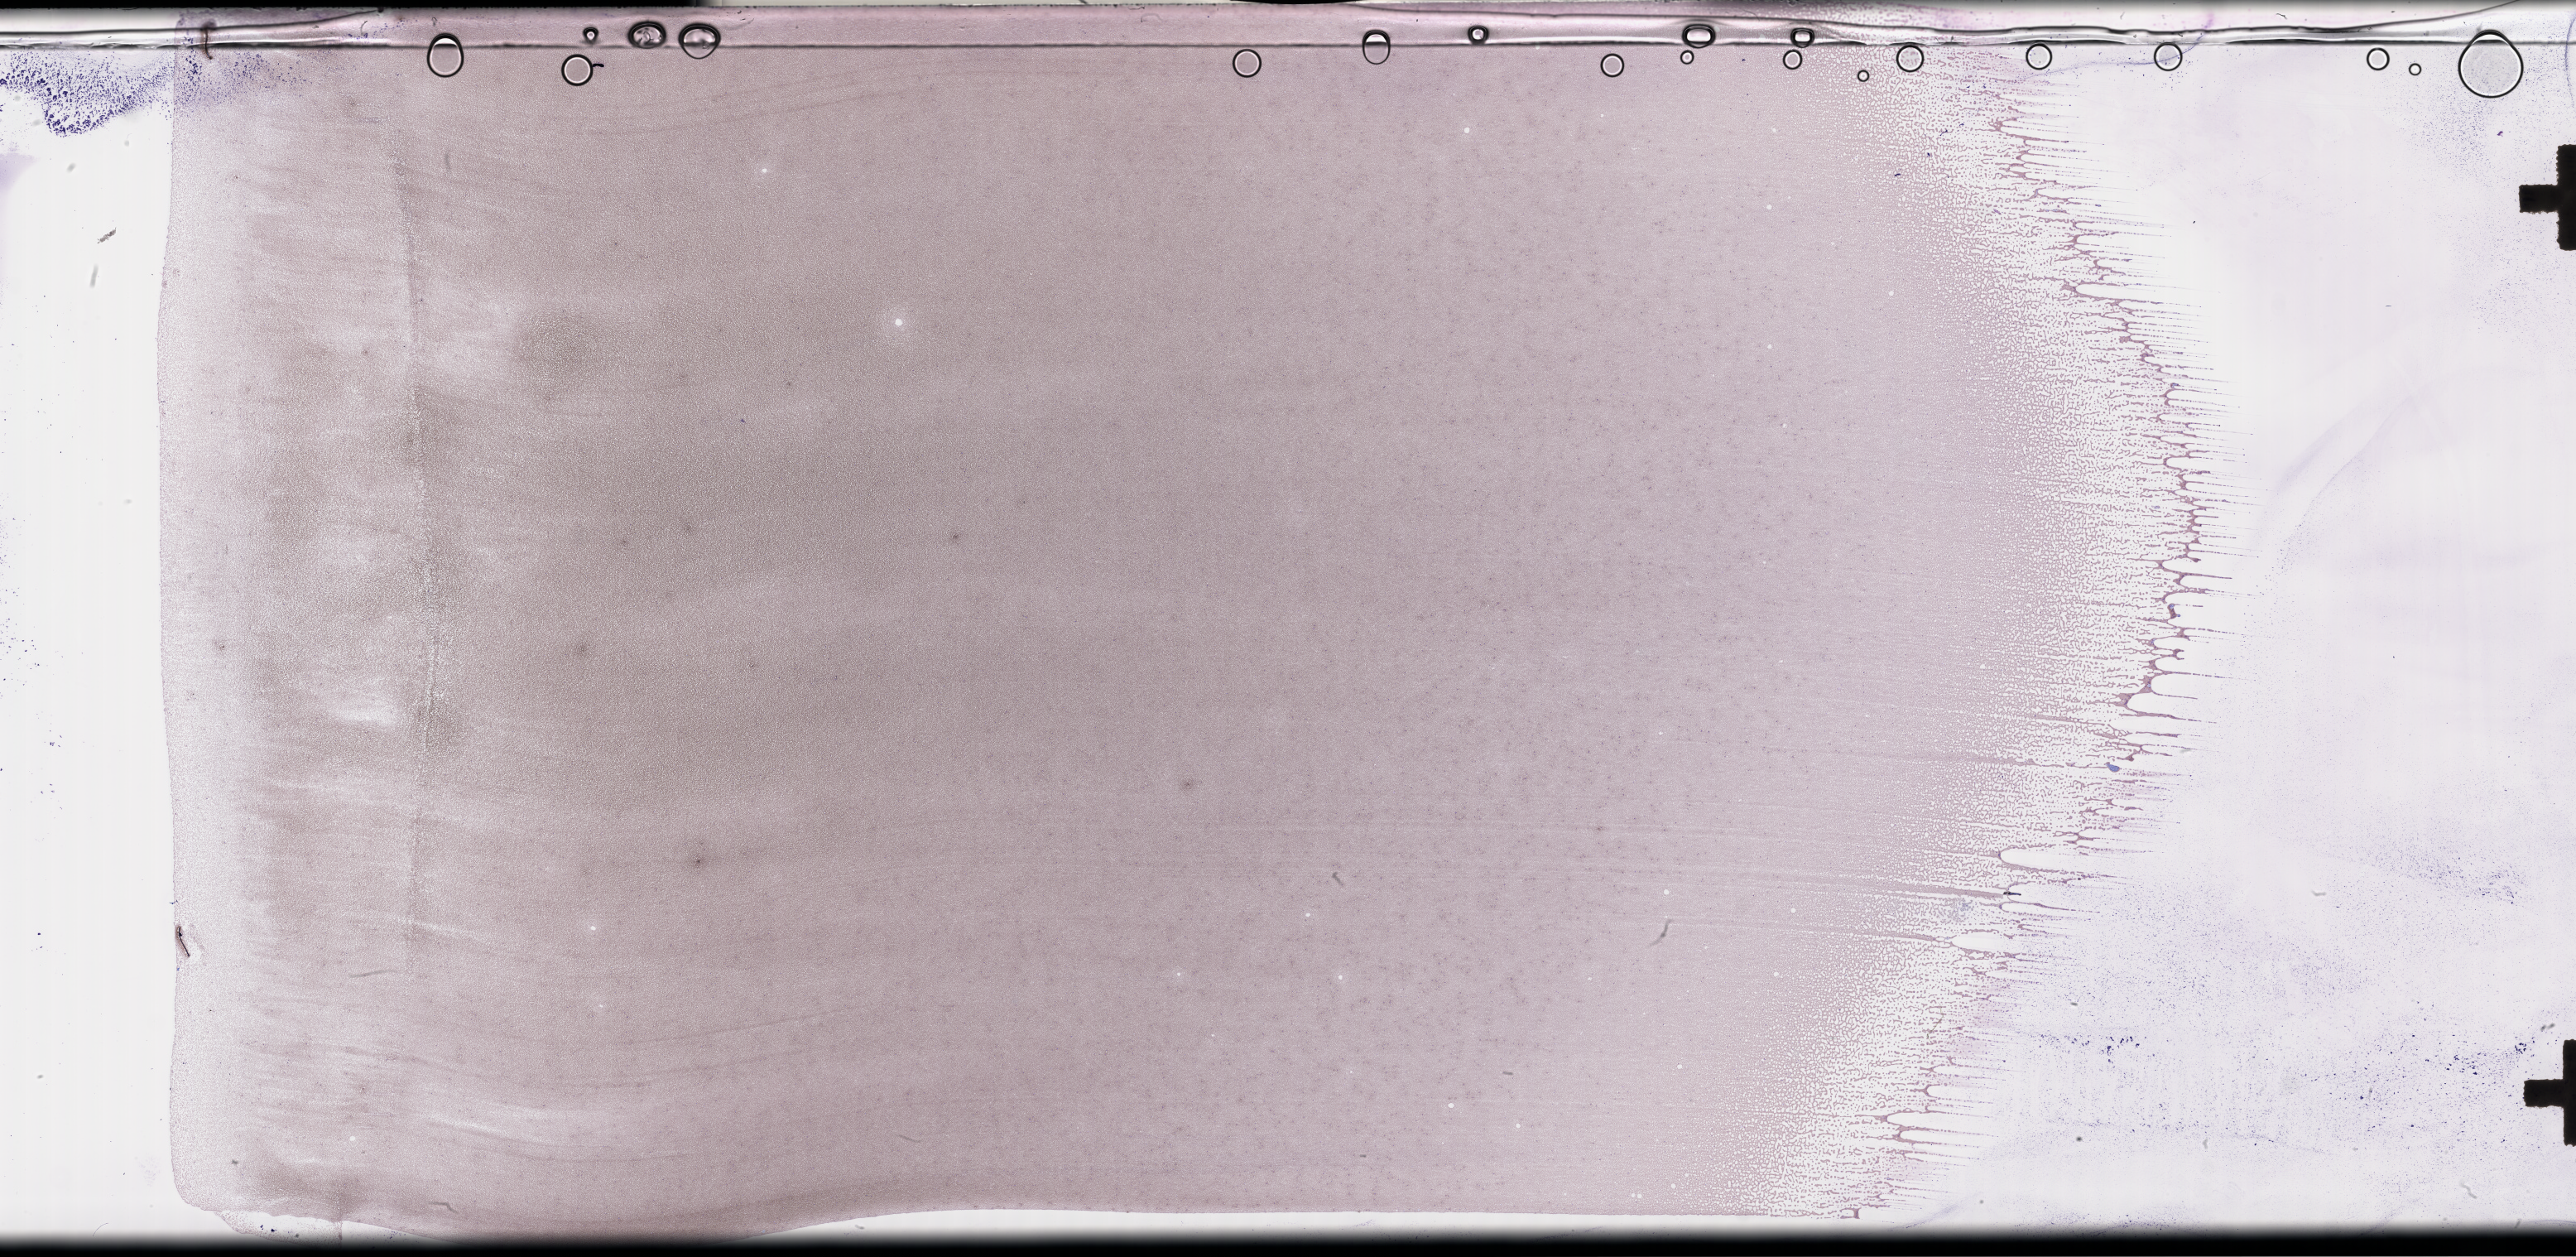
Wright-Giemsa-stained whole blood smear, whole-slide image, low-resolution overview of the scanned area, about 50.3 x 24.5 mm, EDTA-anticoagulated smear, specimen time point: collected at disease progression. Female patient.
- patient diagnosis: Plasma Cell Myeloma